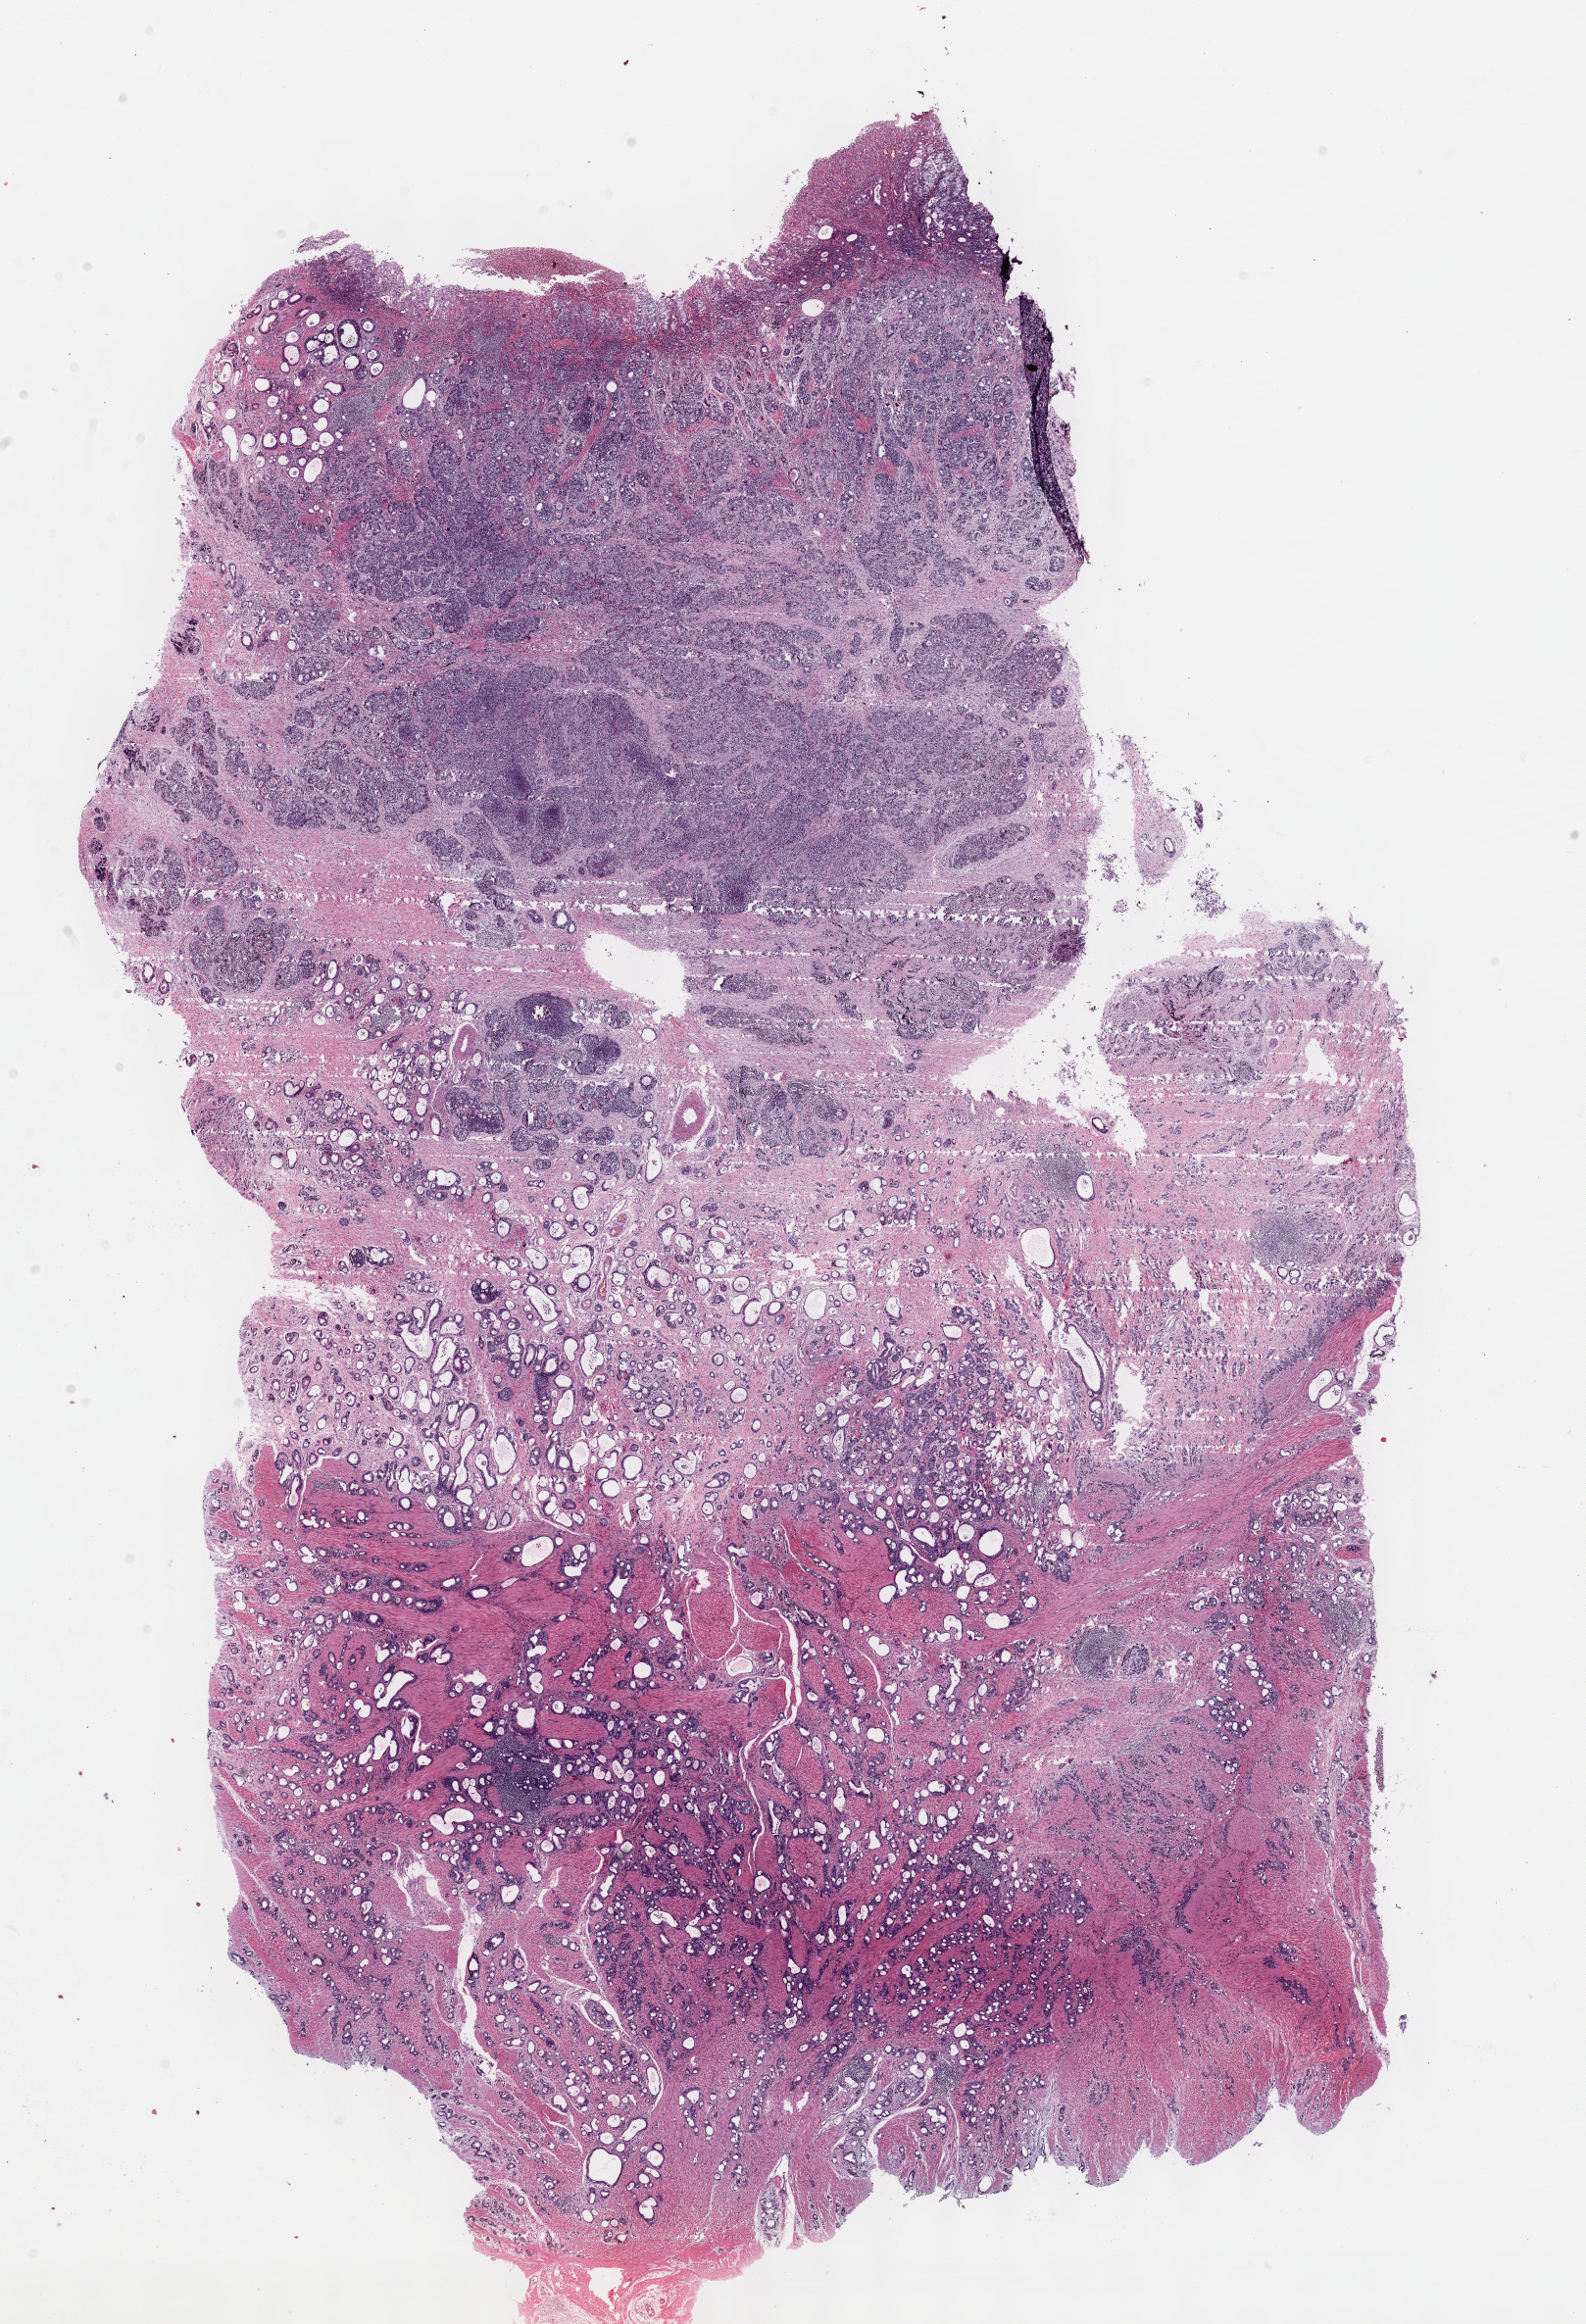
H&E-stained whole-slide image, low-resolution overview of the scanned area, about 13.1 x 19.2 mm (slide scanned at 40x); formalin-fixed paraffin-embedded (FFPE) diagnostic section; sample: primary tumour, stomach. Male patient; age at initial diagnosis 48 years.
Histologic diagnosis: Adenocarcinoma, NOS (gastric antrum).